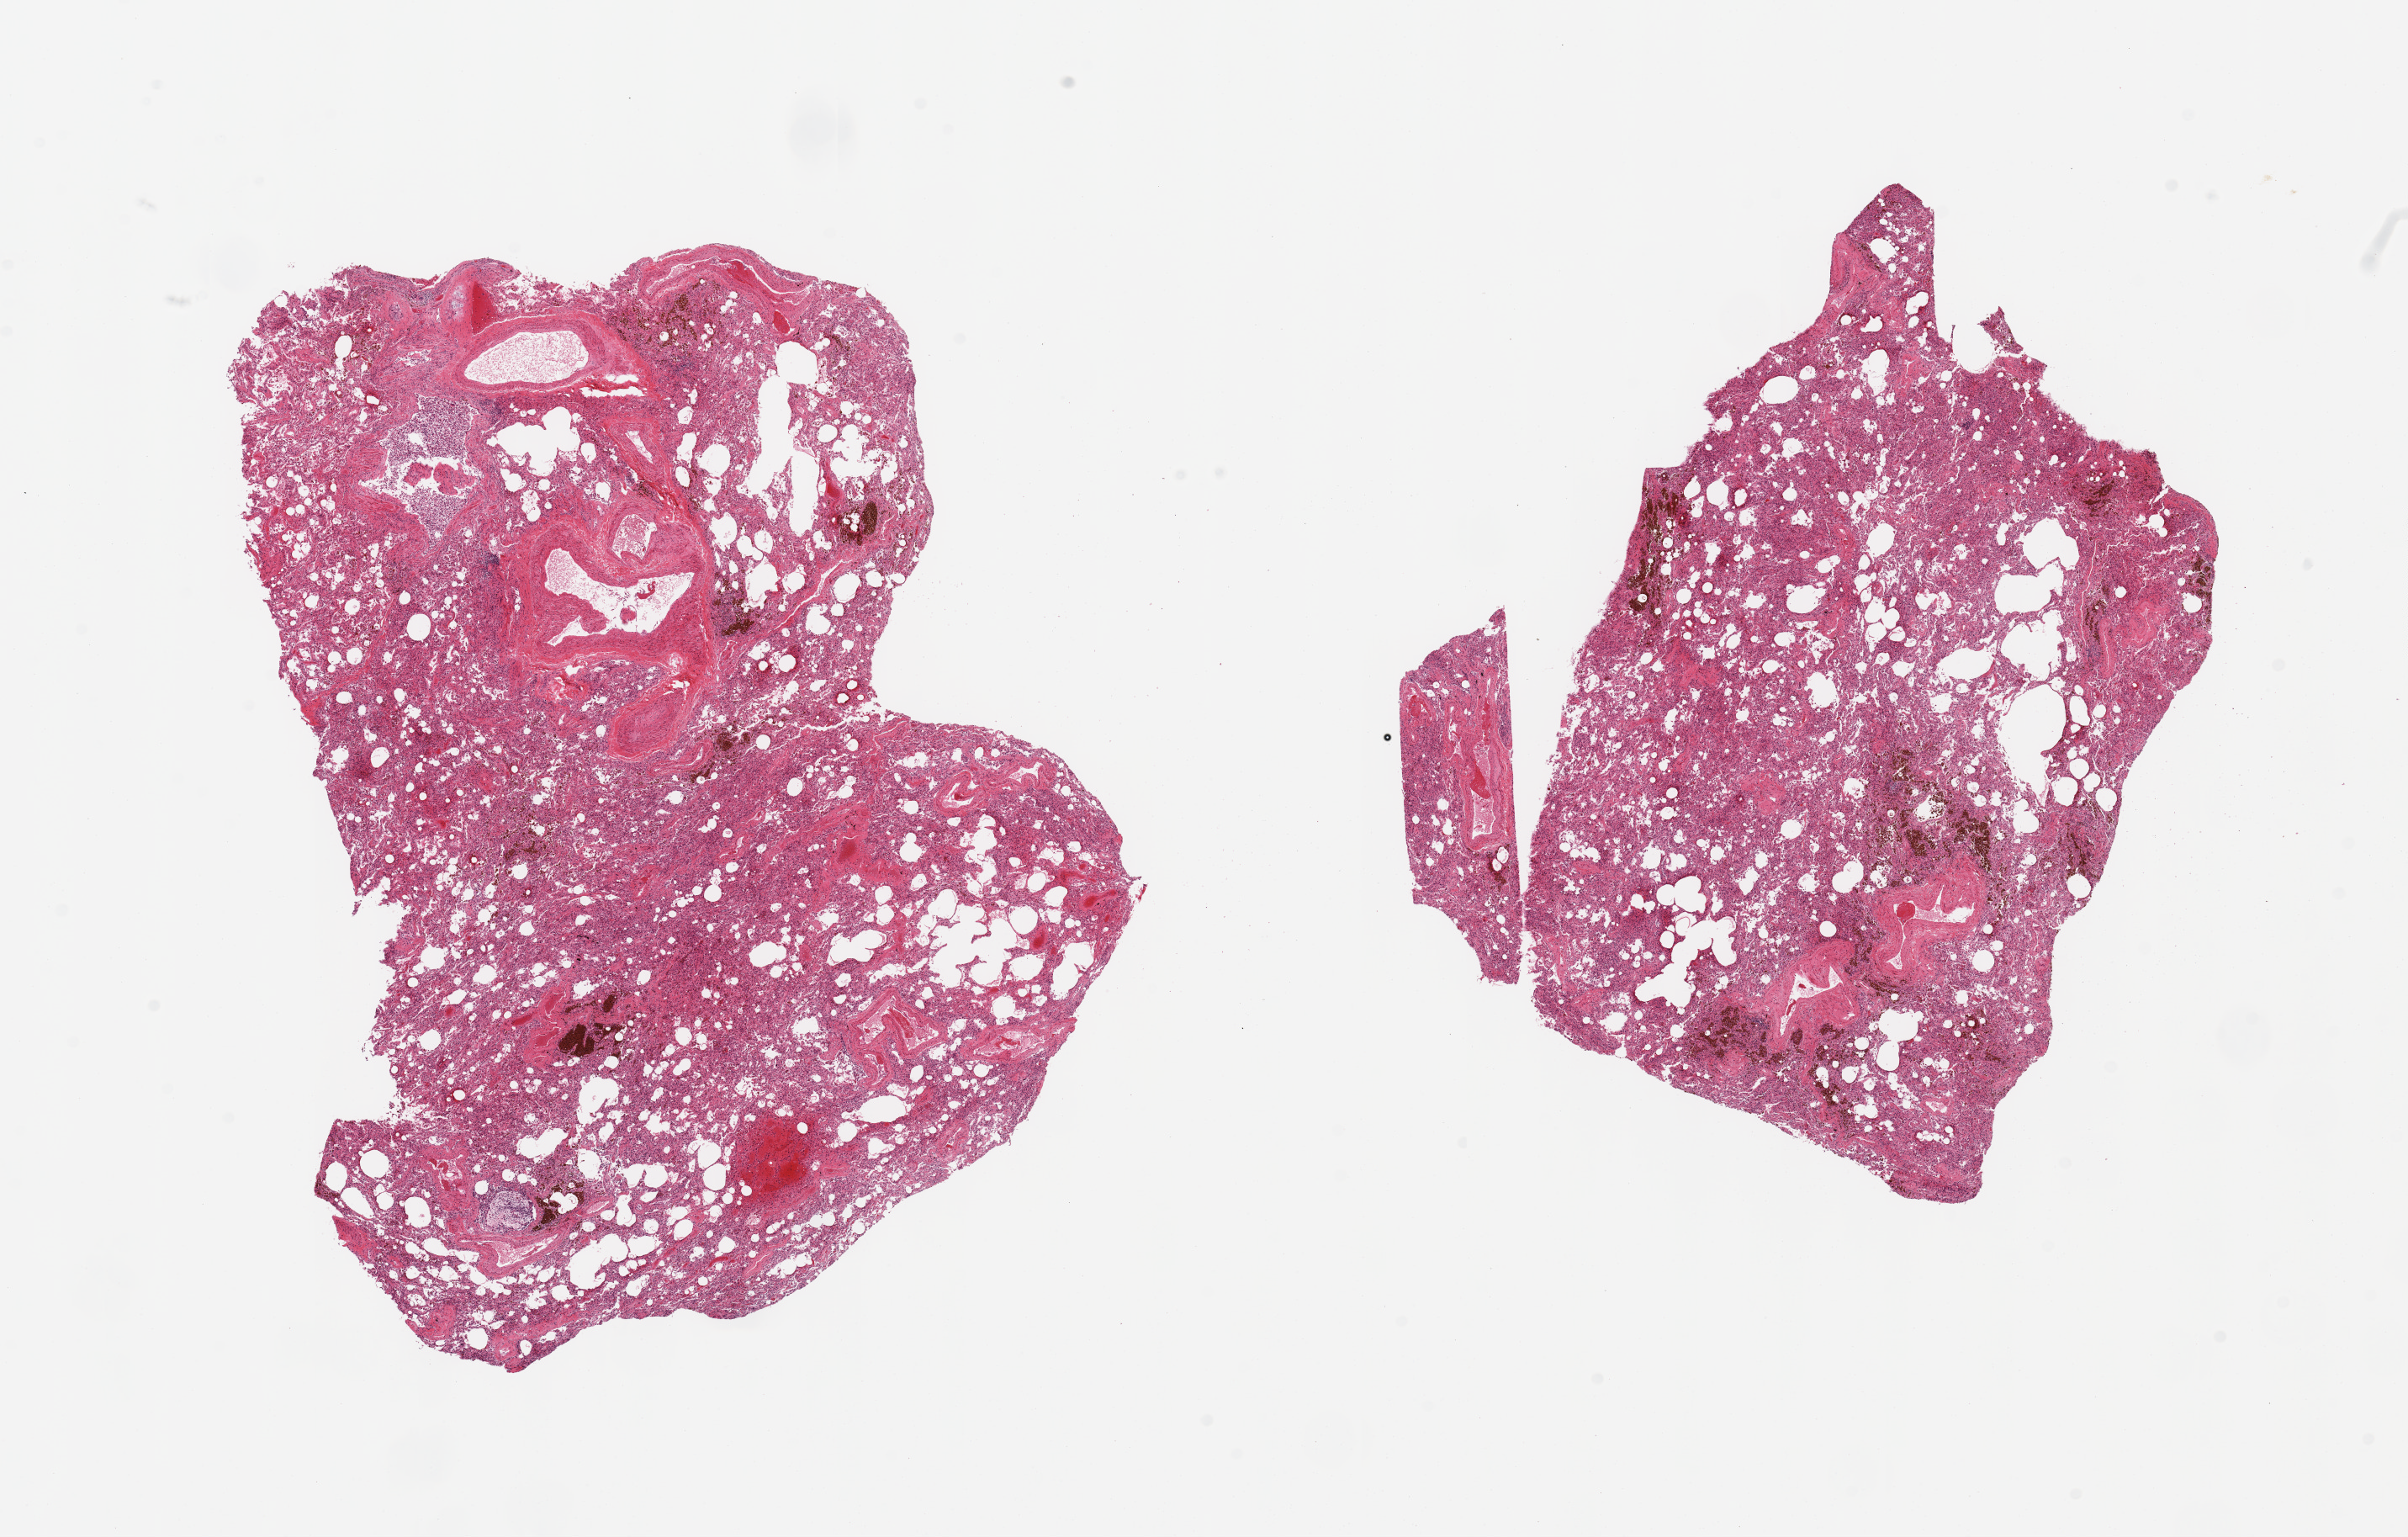
Whole-slide image, H&E stain, a low-resolution overview of the entire scanned area, about 22.6 x 14.4 mm (from a 20x scan); PAXgene-fixed paraffin-embedded (PFPE) section; sampled site (target tissue): lung; donor tissue sample. Donor sex: male.
• review note (as recorded): 2 pieces; fibrosis, numerous hemosiderin-laden macrophages, focus of cartilage, atelectasis